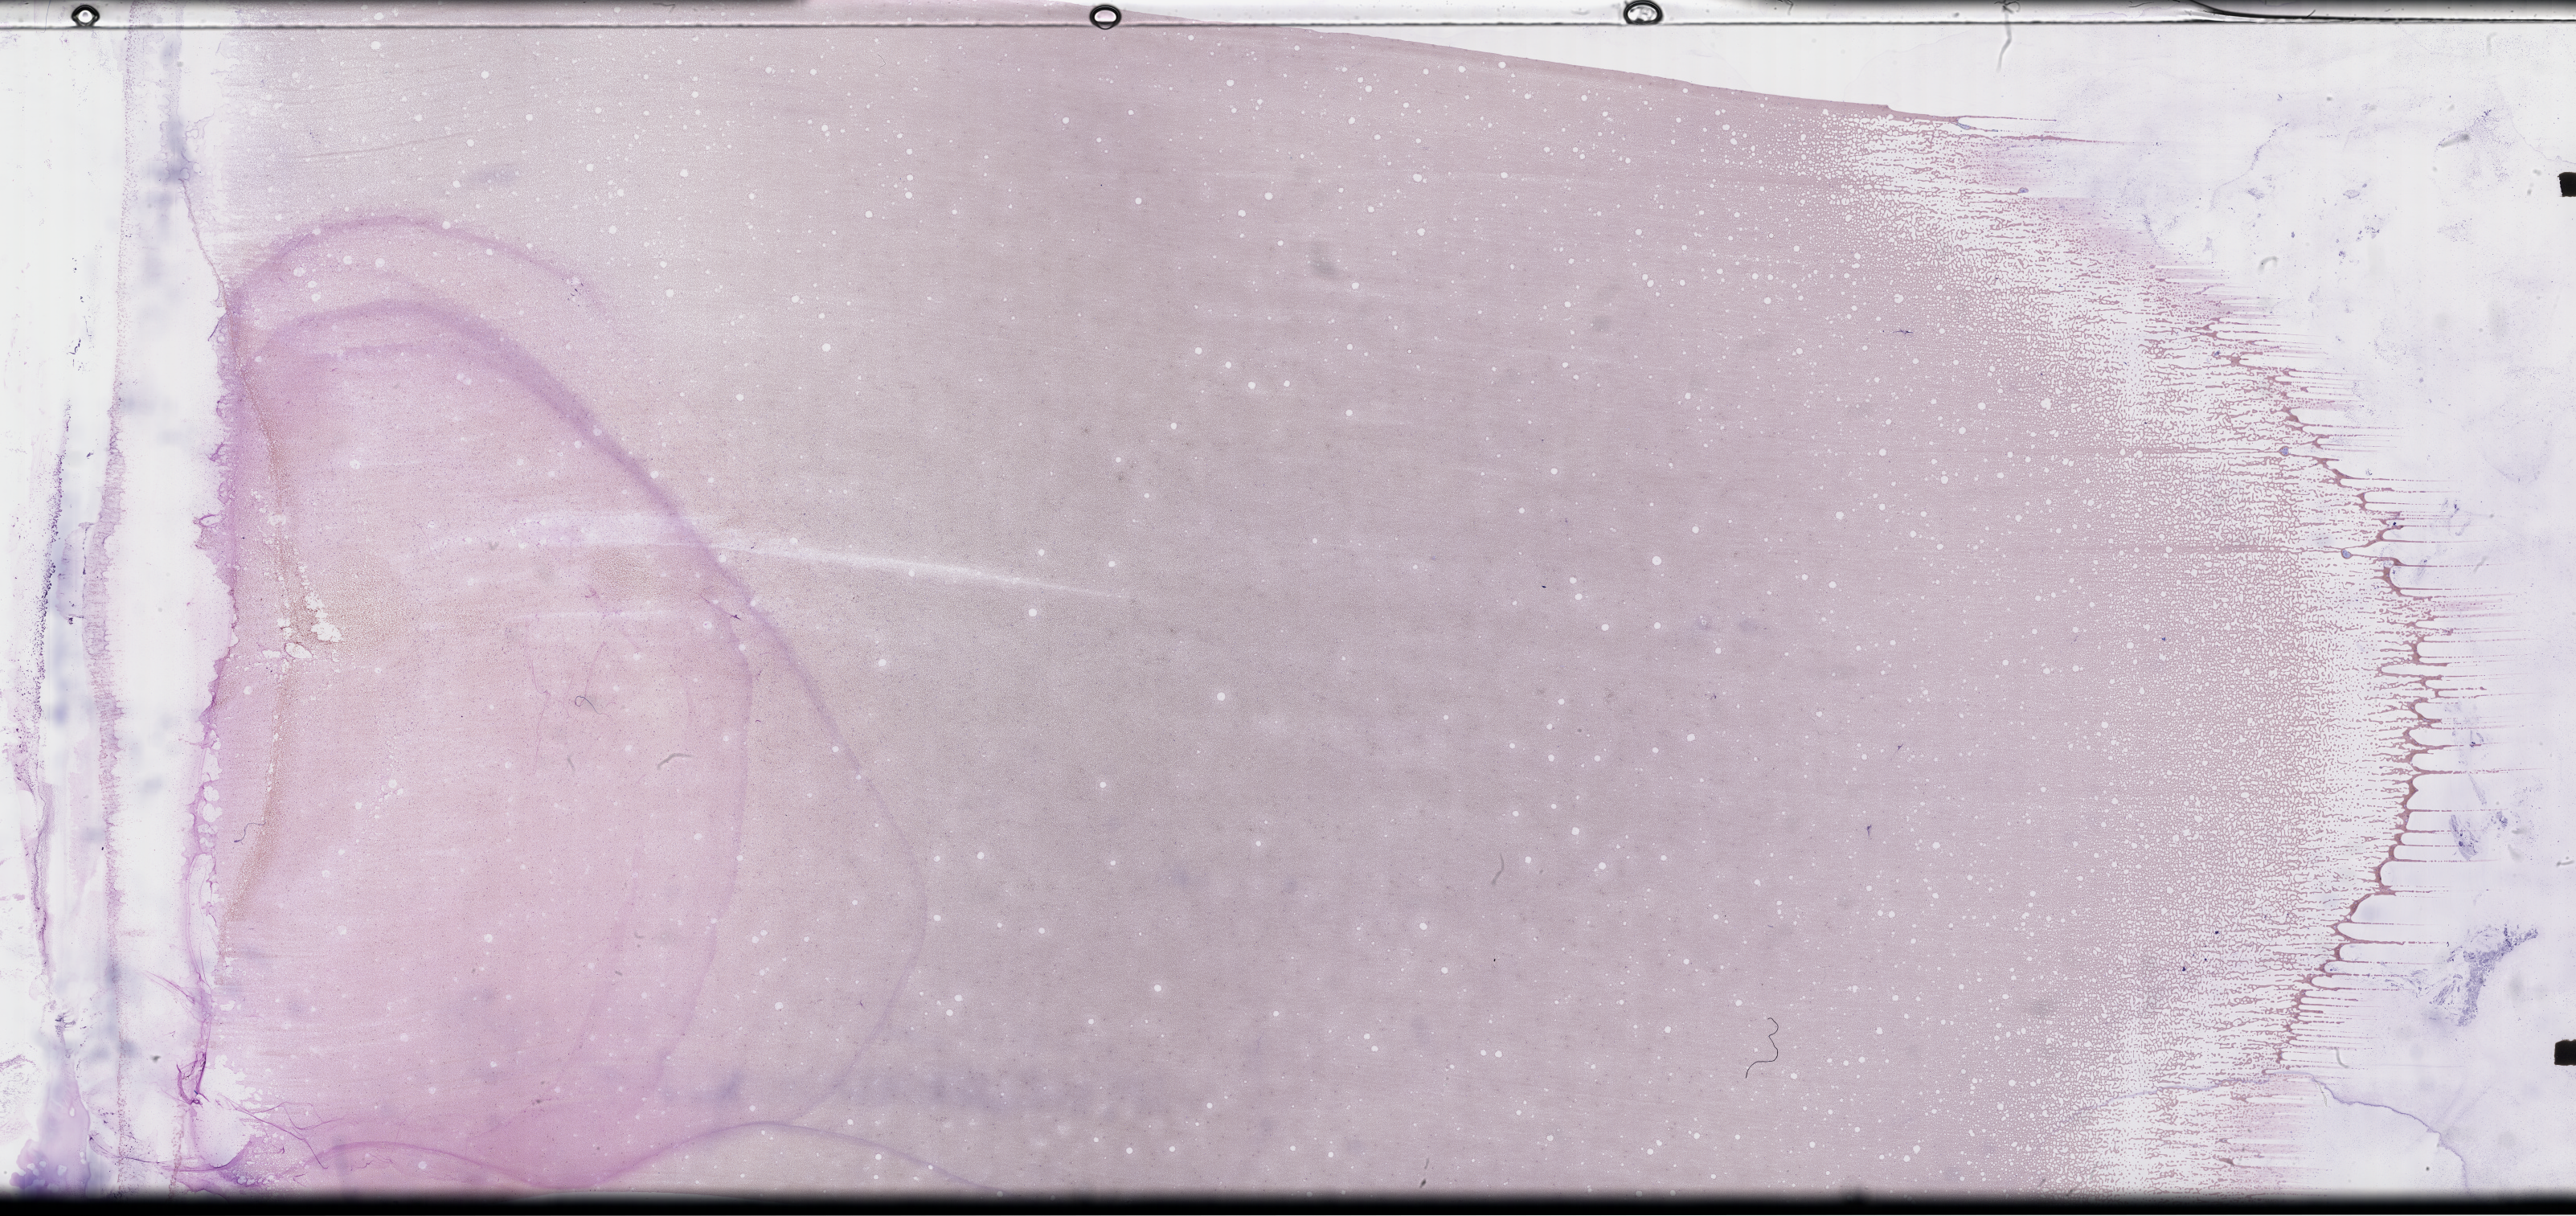
Whole-slide image of a whole blood smear, Wright-Giemsa stain, a low-resolution overview of the entire scanned area, about 51.8 x 24.4 mm, specimen time point: collected on treatment. Male patient.
• from a patient with: Plasma Cell Myeloma